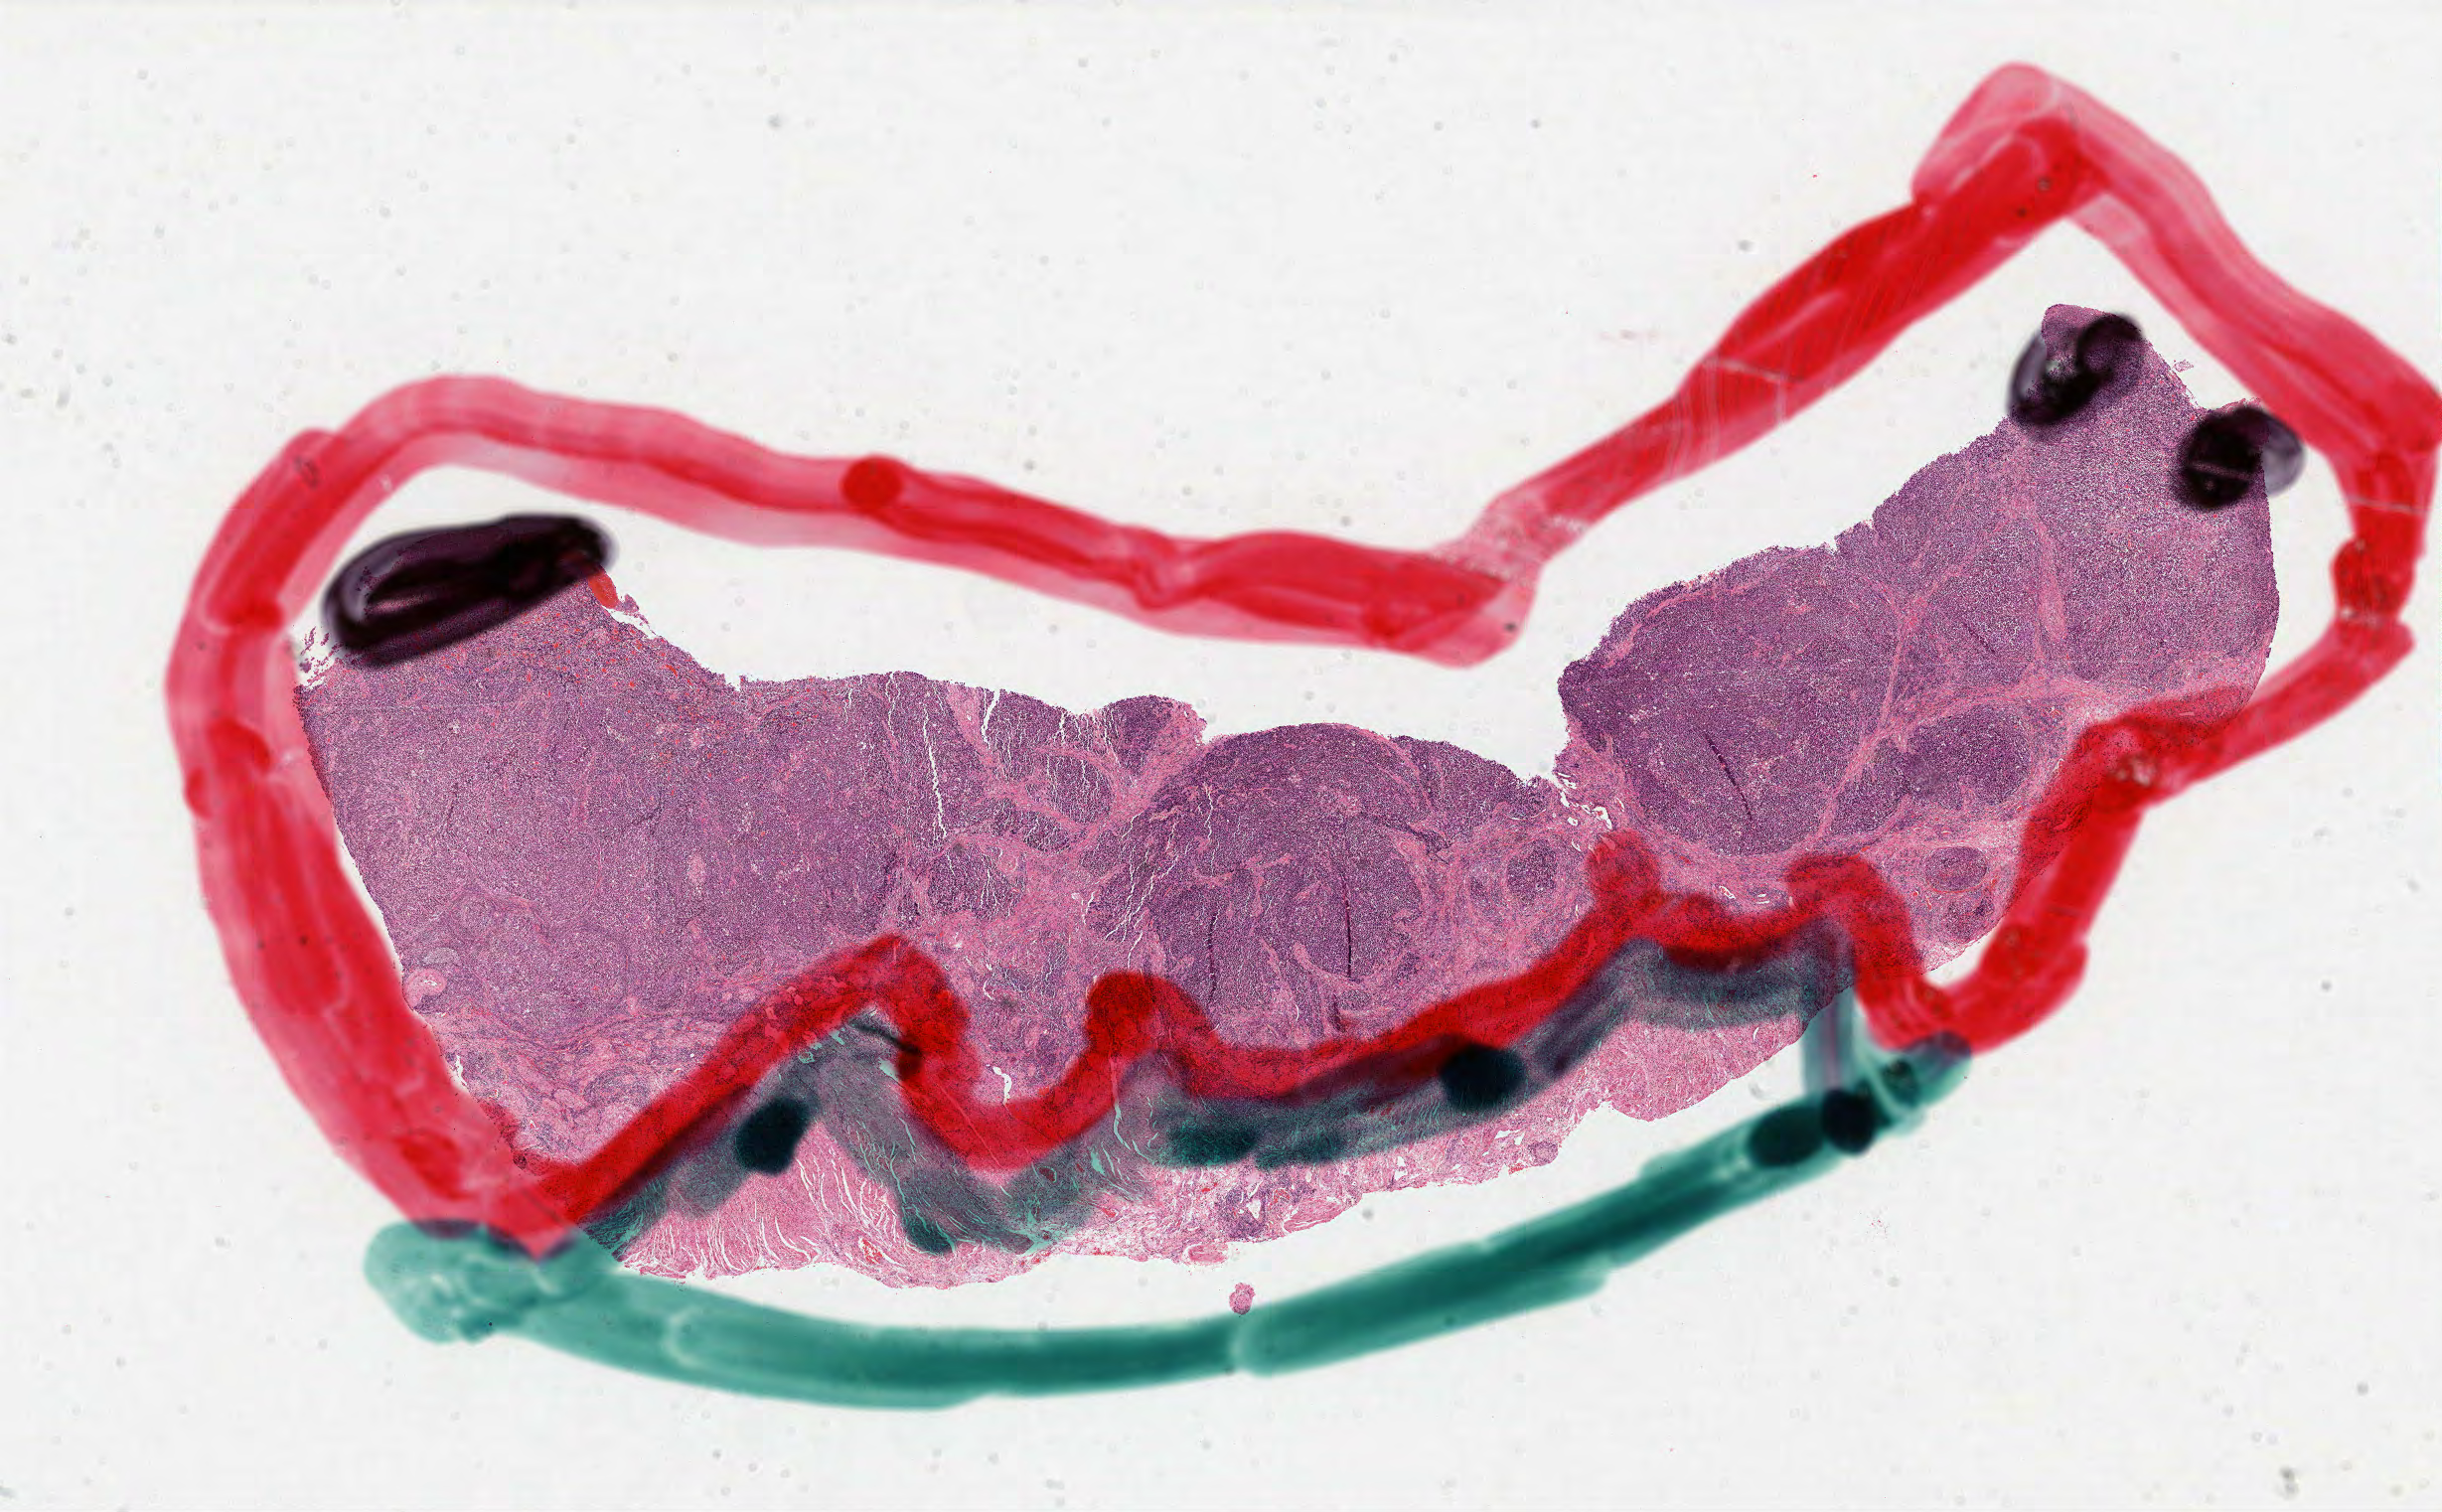
Digitized H&E tissue section (whole slide) — a low-resolution overview of the entire scanned area, about 19.8 x 12.3 mm, FFPE section, stomach, primary tumour sample. Patient: female, age at initial diagnosis 75 years. Histologic grade: G3 (poorly differentiated).
Pathologic diagnosis: Adenocarcinoma, NOS (cardia, NOS). AJCC pathologic stage: IIB. TNM: T2 N2 M0. Lymph nodes positive (case pathology): 4 of 4 examined.